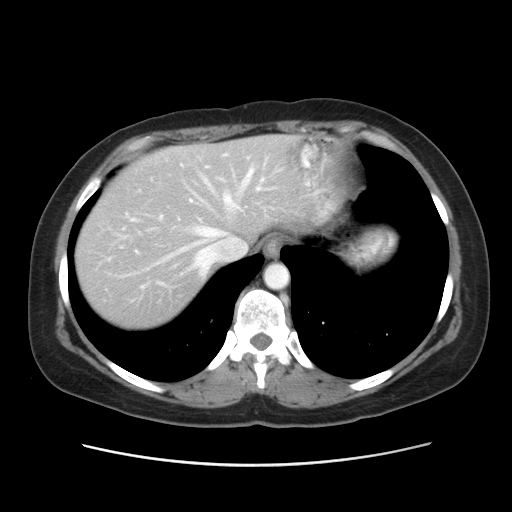
Contrast-enhanced abdominal CT, one axial slice; position 42 of 52 along the scan axis; intravenous contrast given; soft-tissue window (W 400 / L 40 HU); 512 × 512 image matrix, field of view 362 × 362 mm. Female patient, age 48 years. Case-level facts recorded for this patient, not image findings: diagnosis: colorectal cancer liver metastases, imaged before liver resection; multiple liver metastases: yes; largest metastasis: 4.5 cm.
Annotated regions visible in this slice (manually delineated by an expert):
- hepatic veins: box from (x=121, y=153) to (x=265, y=291) px
- liver: (x=75, y=135)–(x=299, y=327)
- planned liver remnant (the part of the liver to remain after resection): (x=151, y=136)–(x=299, y=241)
- portal vein (with intrahepatic branches): (x=131, y=166)–(x=208, y=252)